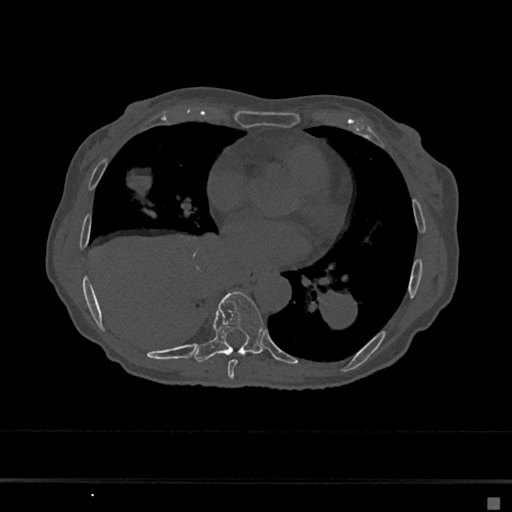
CT including the spine, one axial slice. Slice 336 of 797 in the series (ordered by position). 120 kVp. Bone window (W 1800 / L 400 HU). 0.5 mm slice thickness. 512 × 512 image matrix, field of view 360 × 360 mm. Female patient, age 68 years. From the clinical record (not read from this slice): primary cancer: renal.
Annotated regions visible in this slice (semi-automatic segmentation, software-assisted and operator-edited):
- T7 vertebra: bounding box [x1, y1, x2, y2] px = [228, 359, 238, 379]
- T8 vertebra: [194, 291, 264, 363]